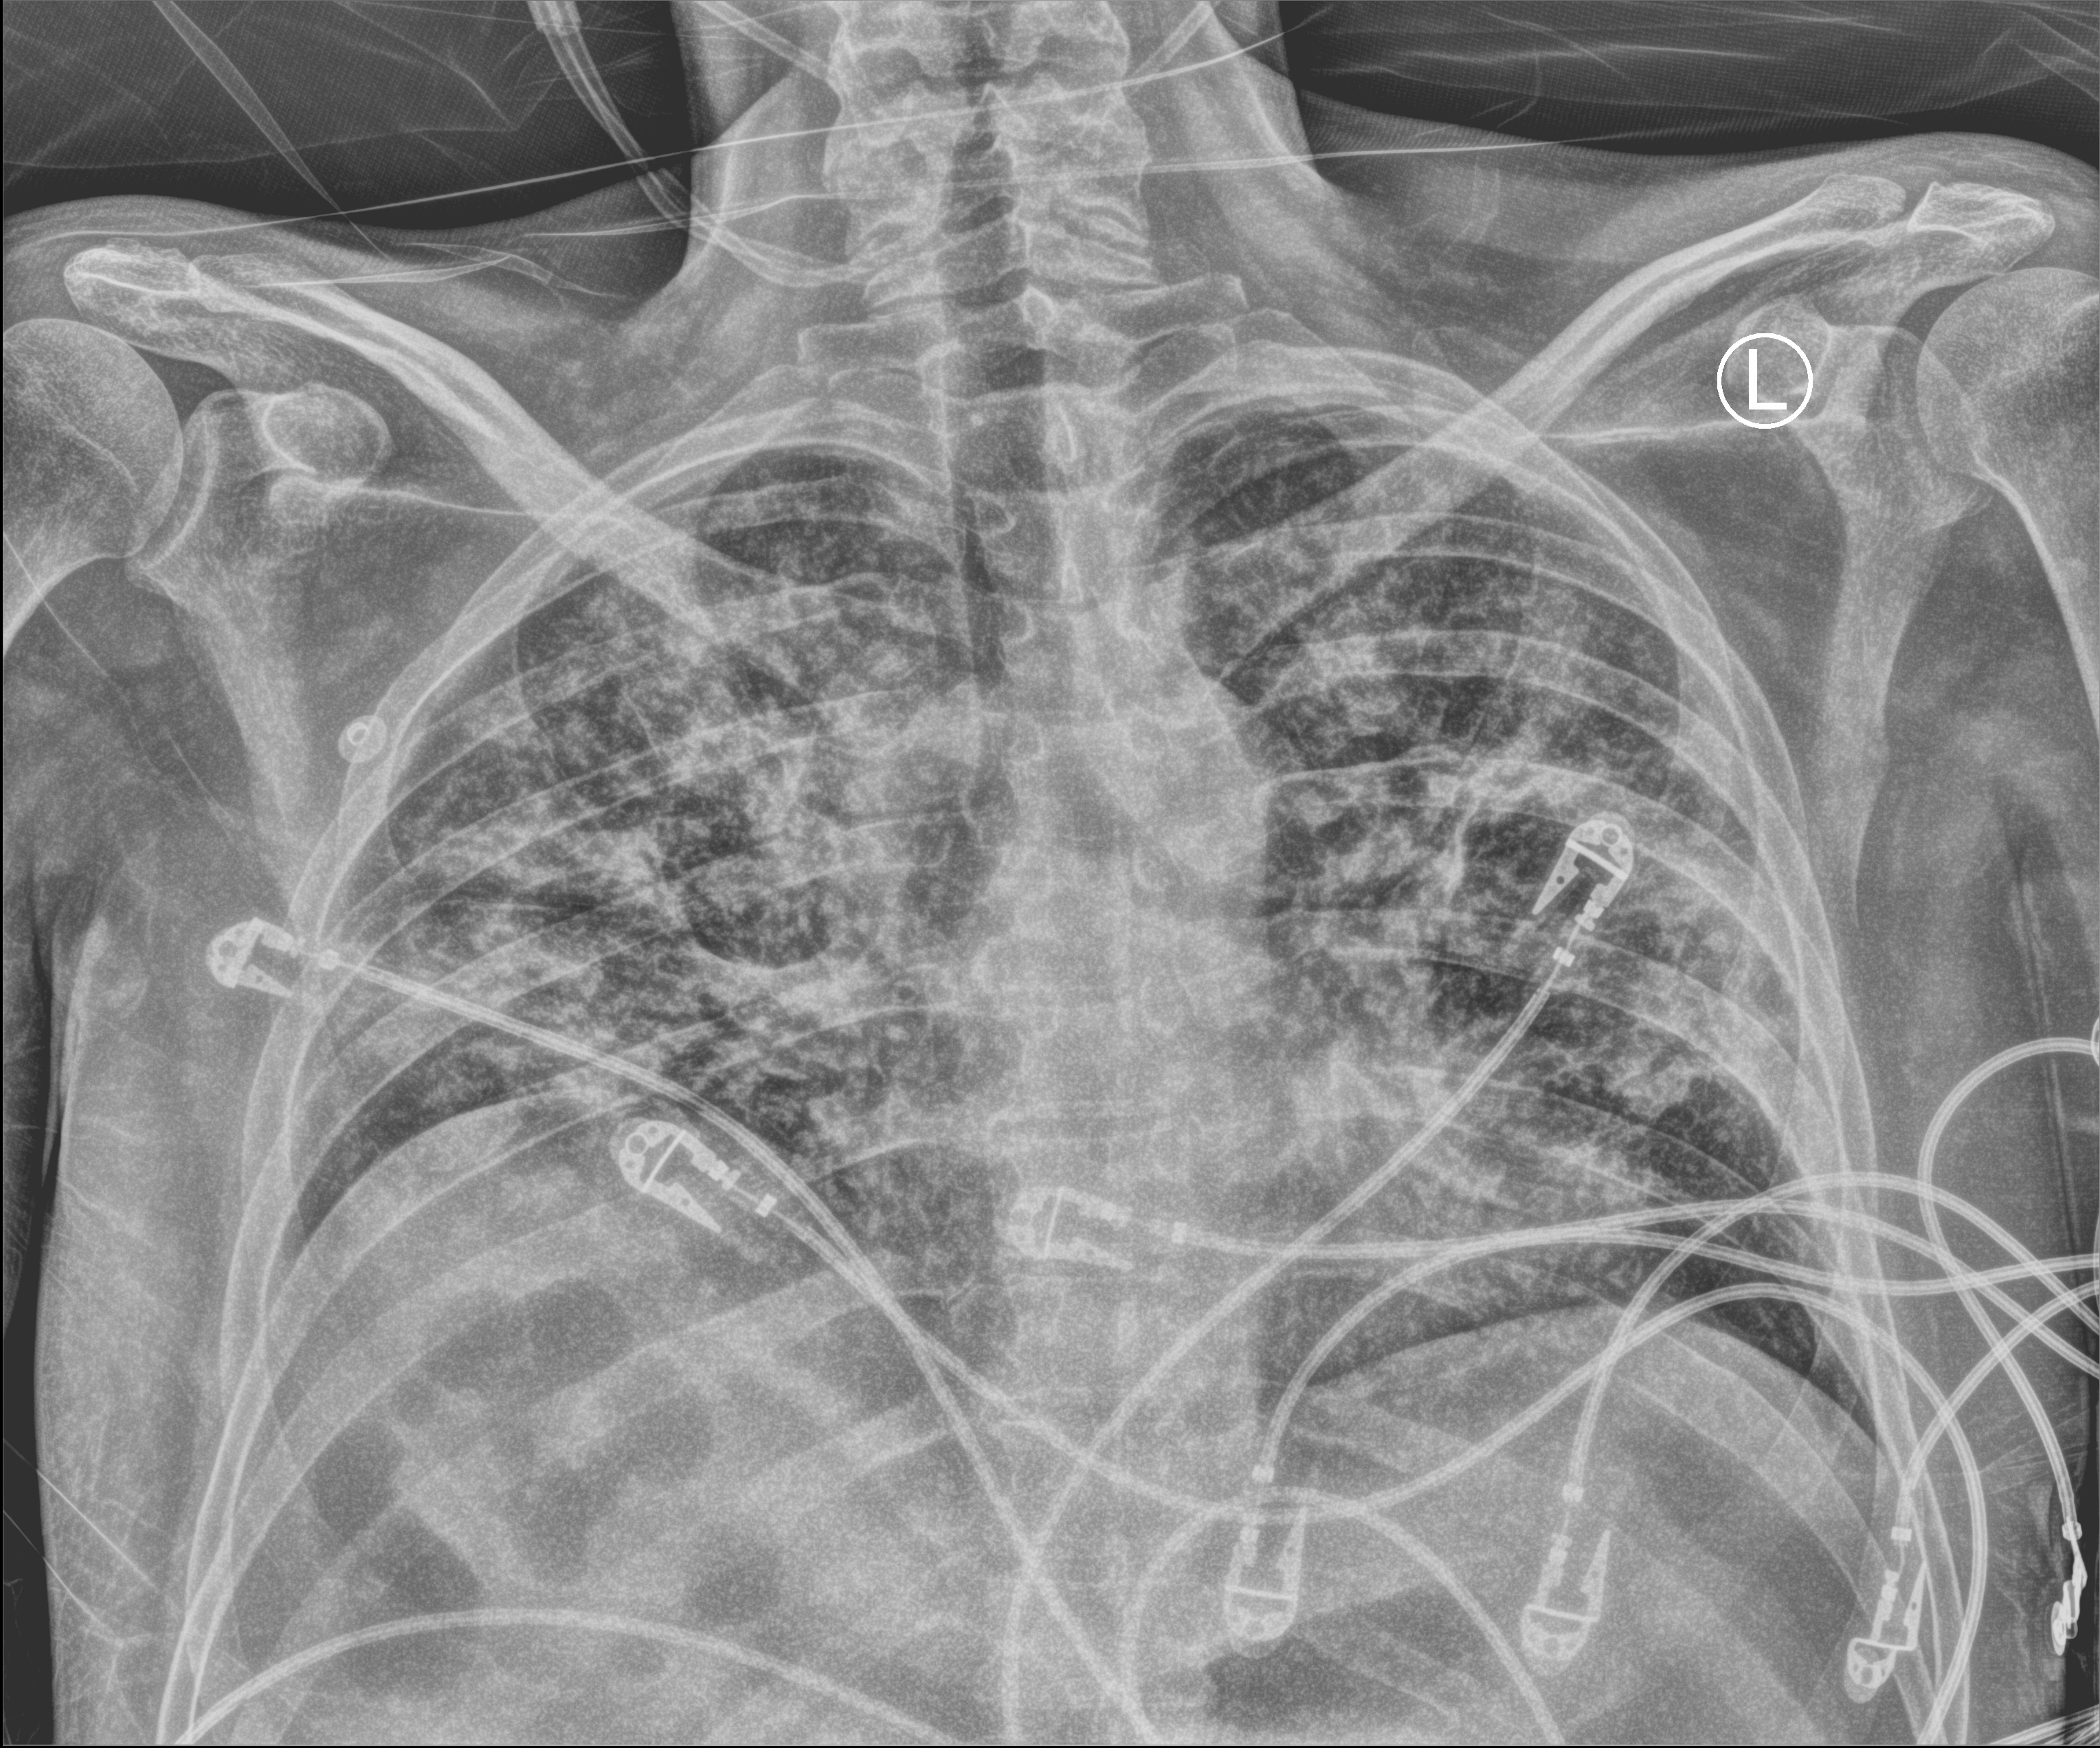
Chest X-ray (portable), anteroposterior (AP) projection. Male patient hospitalised with COVID-19, age 18–59 years.
Admission-level facts for this patient (not findings on this image; timing relative to this image not recorded):
- mechanically ventilated during this hospital stay: yes
- diabetes (admission record): no
- admitted to intensive care during this hospital stay: yes